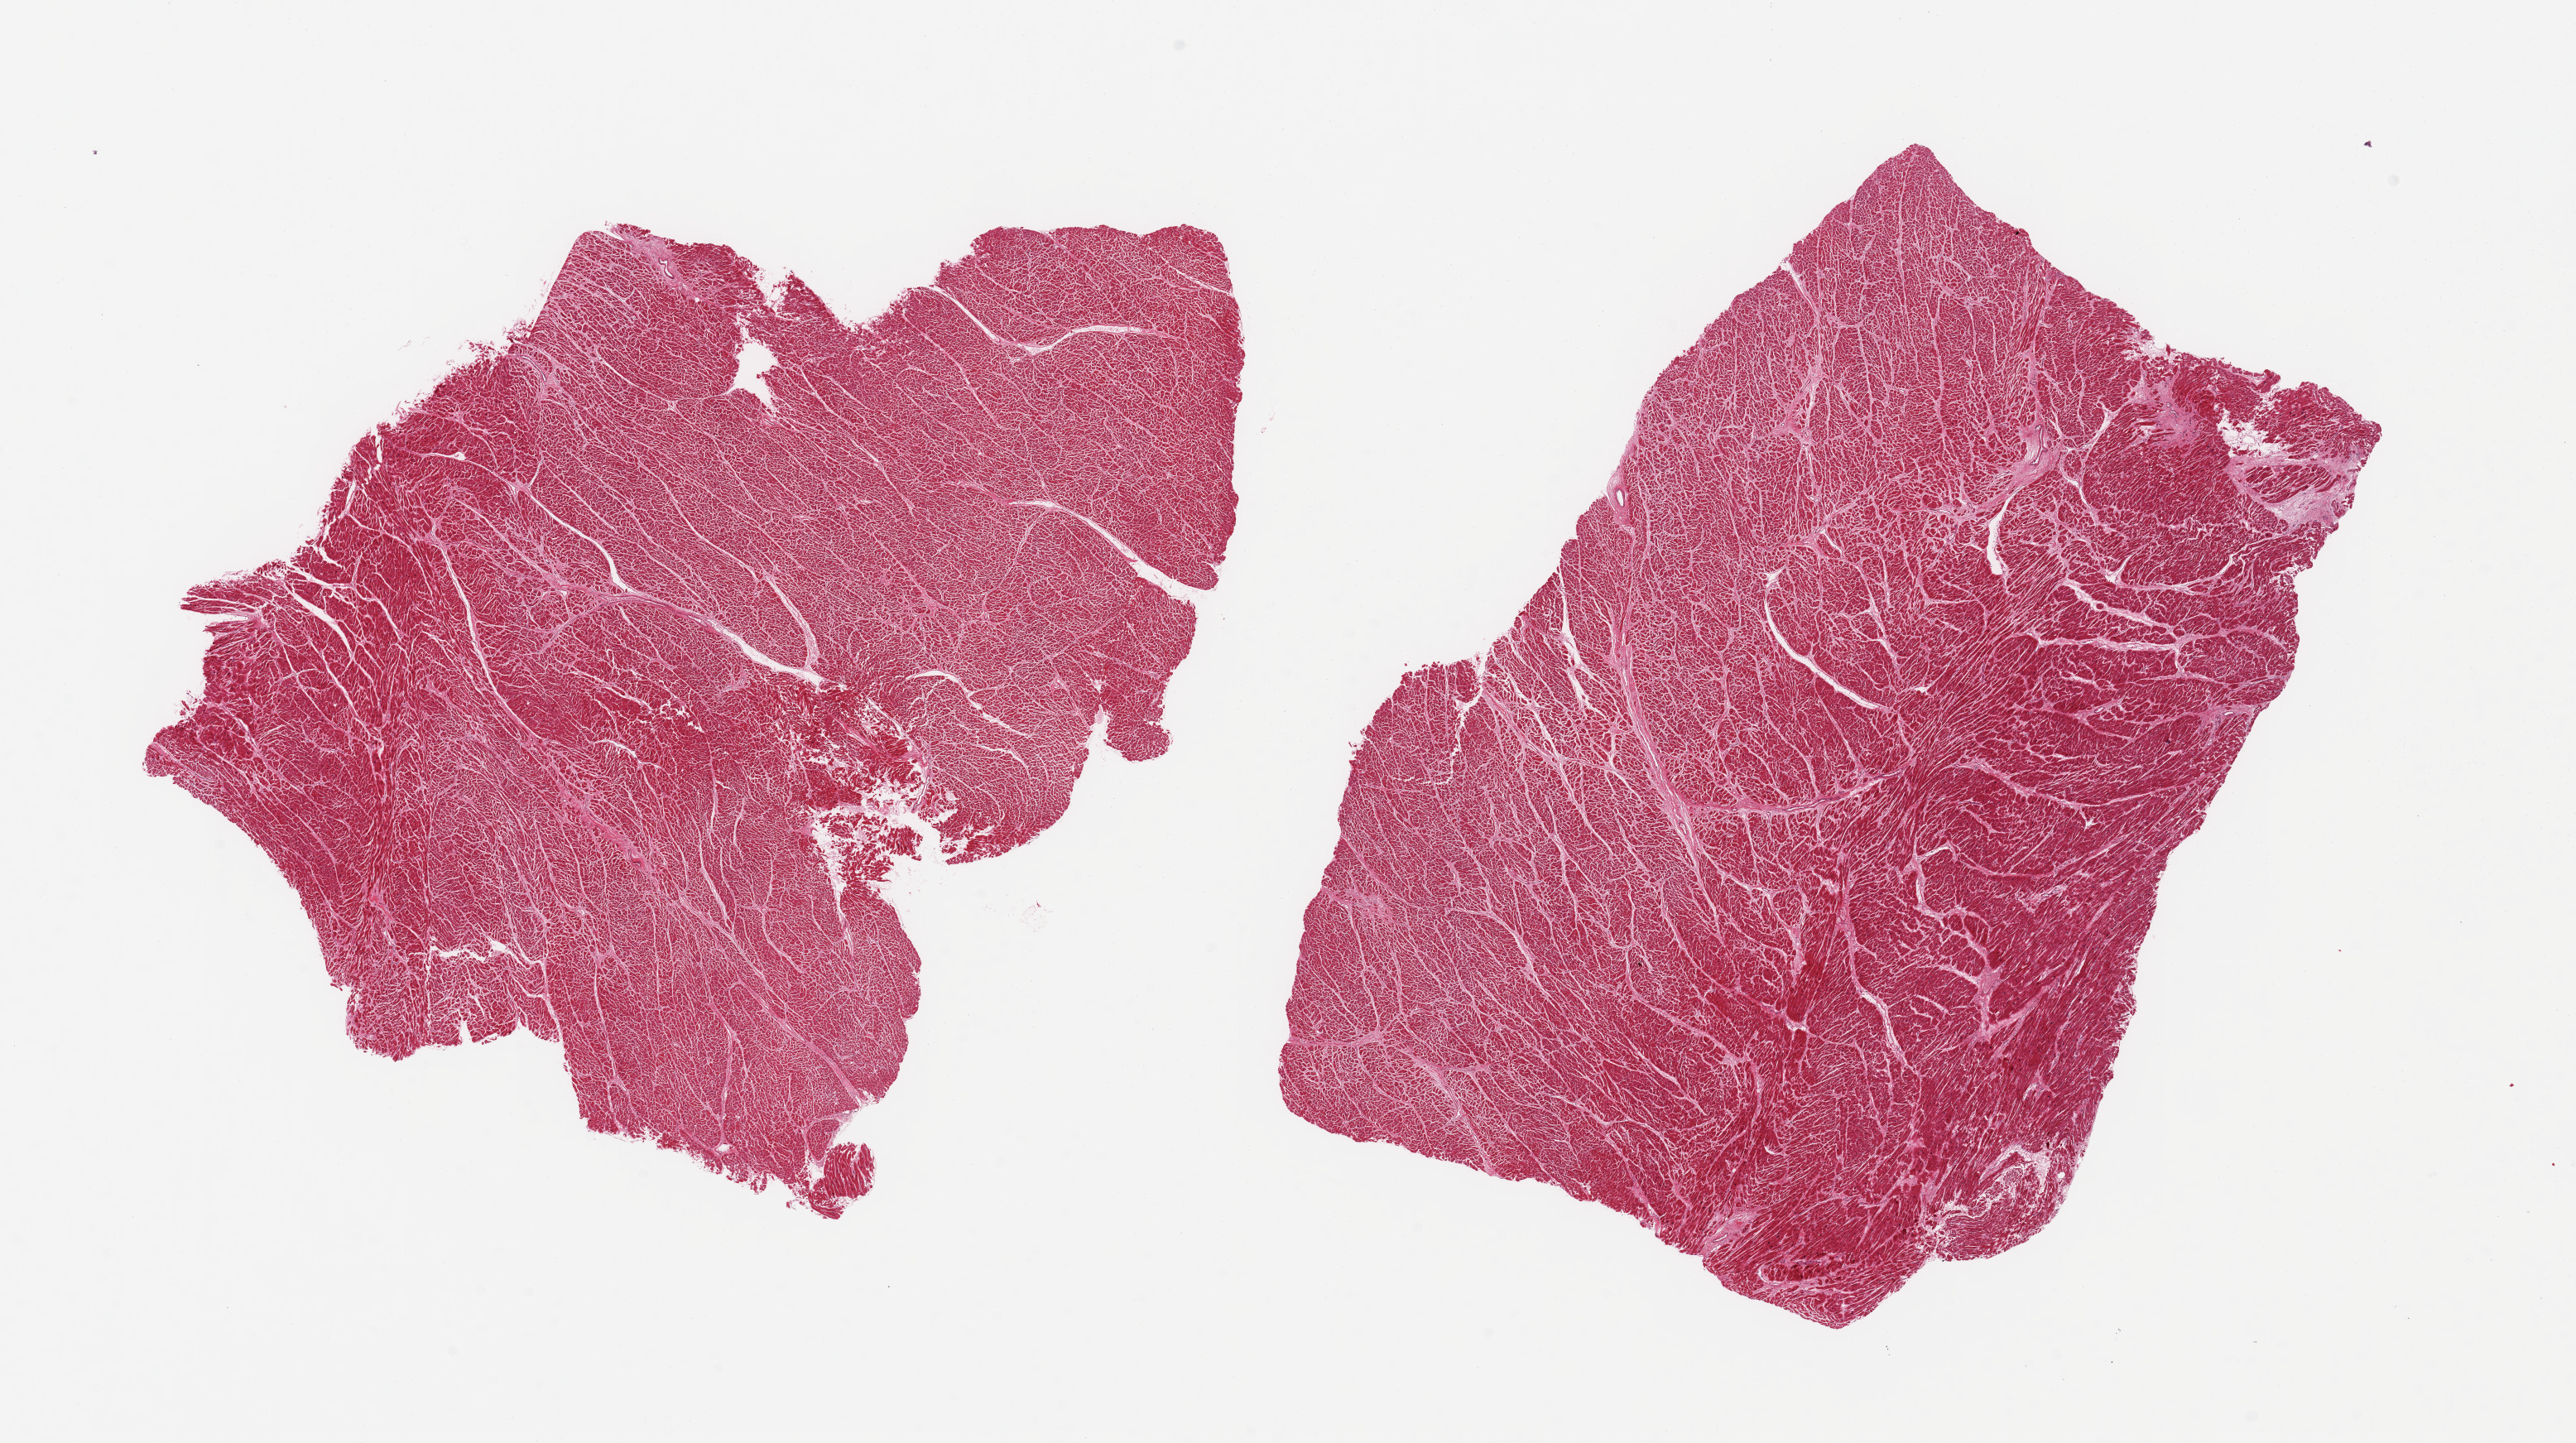
Hematoxylin and eosin (H&E) whole-slide image, shown as a low-resolution overview of the whole scanned area (about 24.6 x 13.8 mm), PAXgene-fixed, paraffin-embedded tissue, target tissue: heart, tissue donor sample. Donor: male.
Review note (as recorded): 2 pieces, moderate interstitial fibrosis/ chronic ischemia.